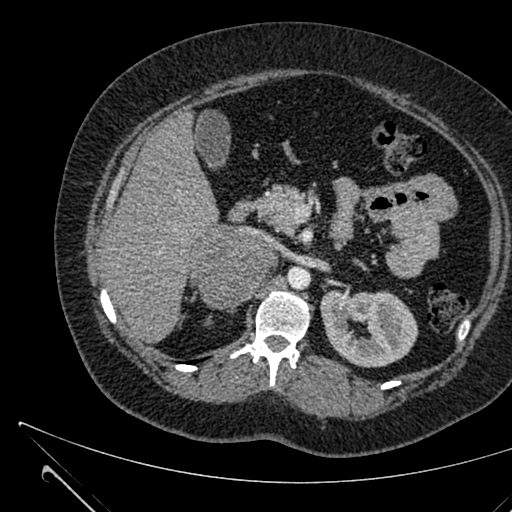
Contrast-enhanced abdominal CT, one axial slice. Position 396 of 731 along the scan axis. 120 kVp. Intravenous contrast given. Soft-tissue window (W 400 / L 40 HU). 1 mm slice thickness. 512 × 512 image matrix. Female patient, age 36 years. Case-level facts recorded for this patient, not image findings: diagnosis: adrenocortical carcinoma; tumour side: right adrenal; tumour size at pathology: 10 cm; Ki-67 index: 20 %; stage (as recorded): 4.
Outlined on this slice (semi-automatically segmented with operator editing):
- mass: bounding box [x1, y1, x2, y2] px = [191, 227, 277, 306]